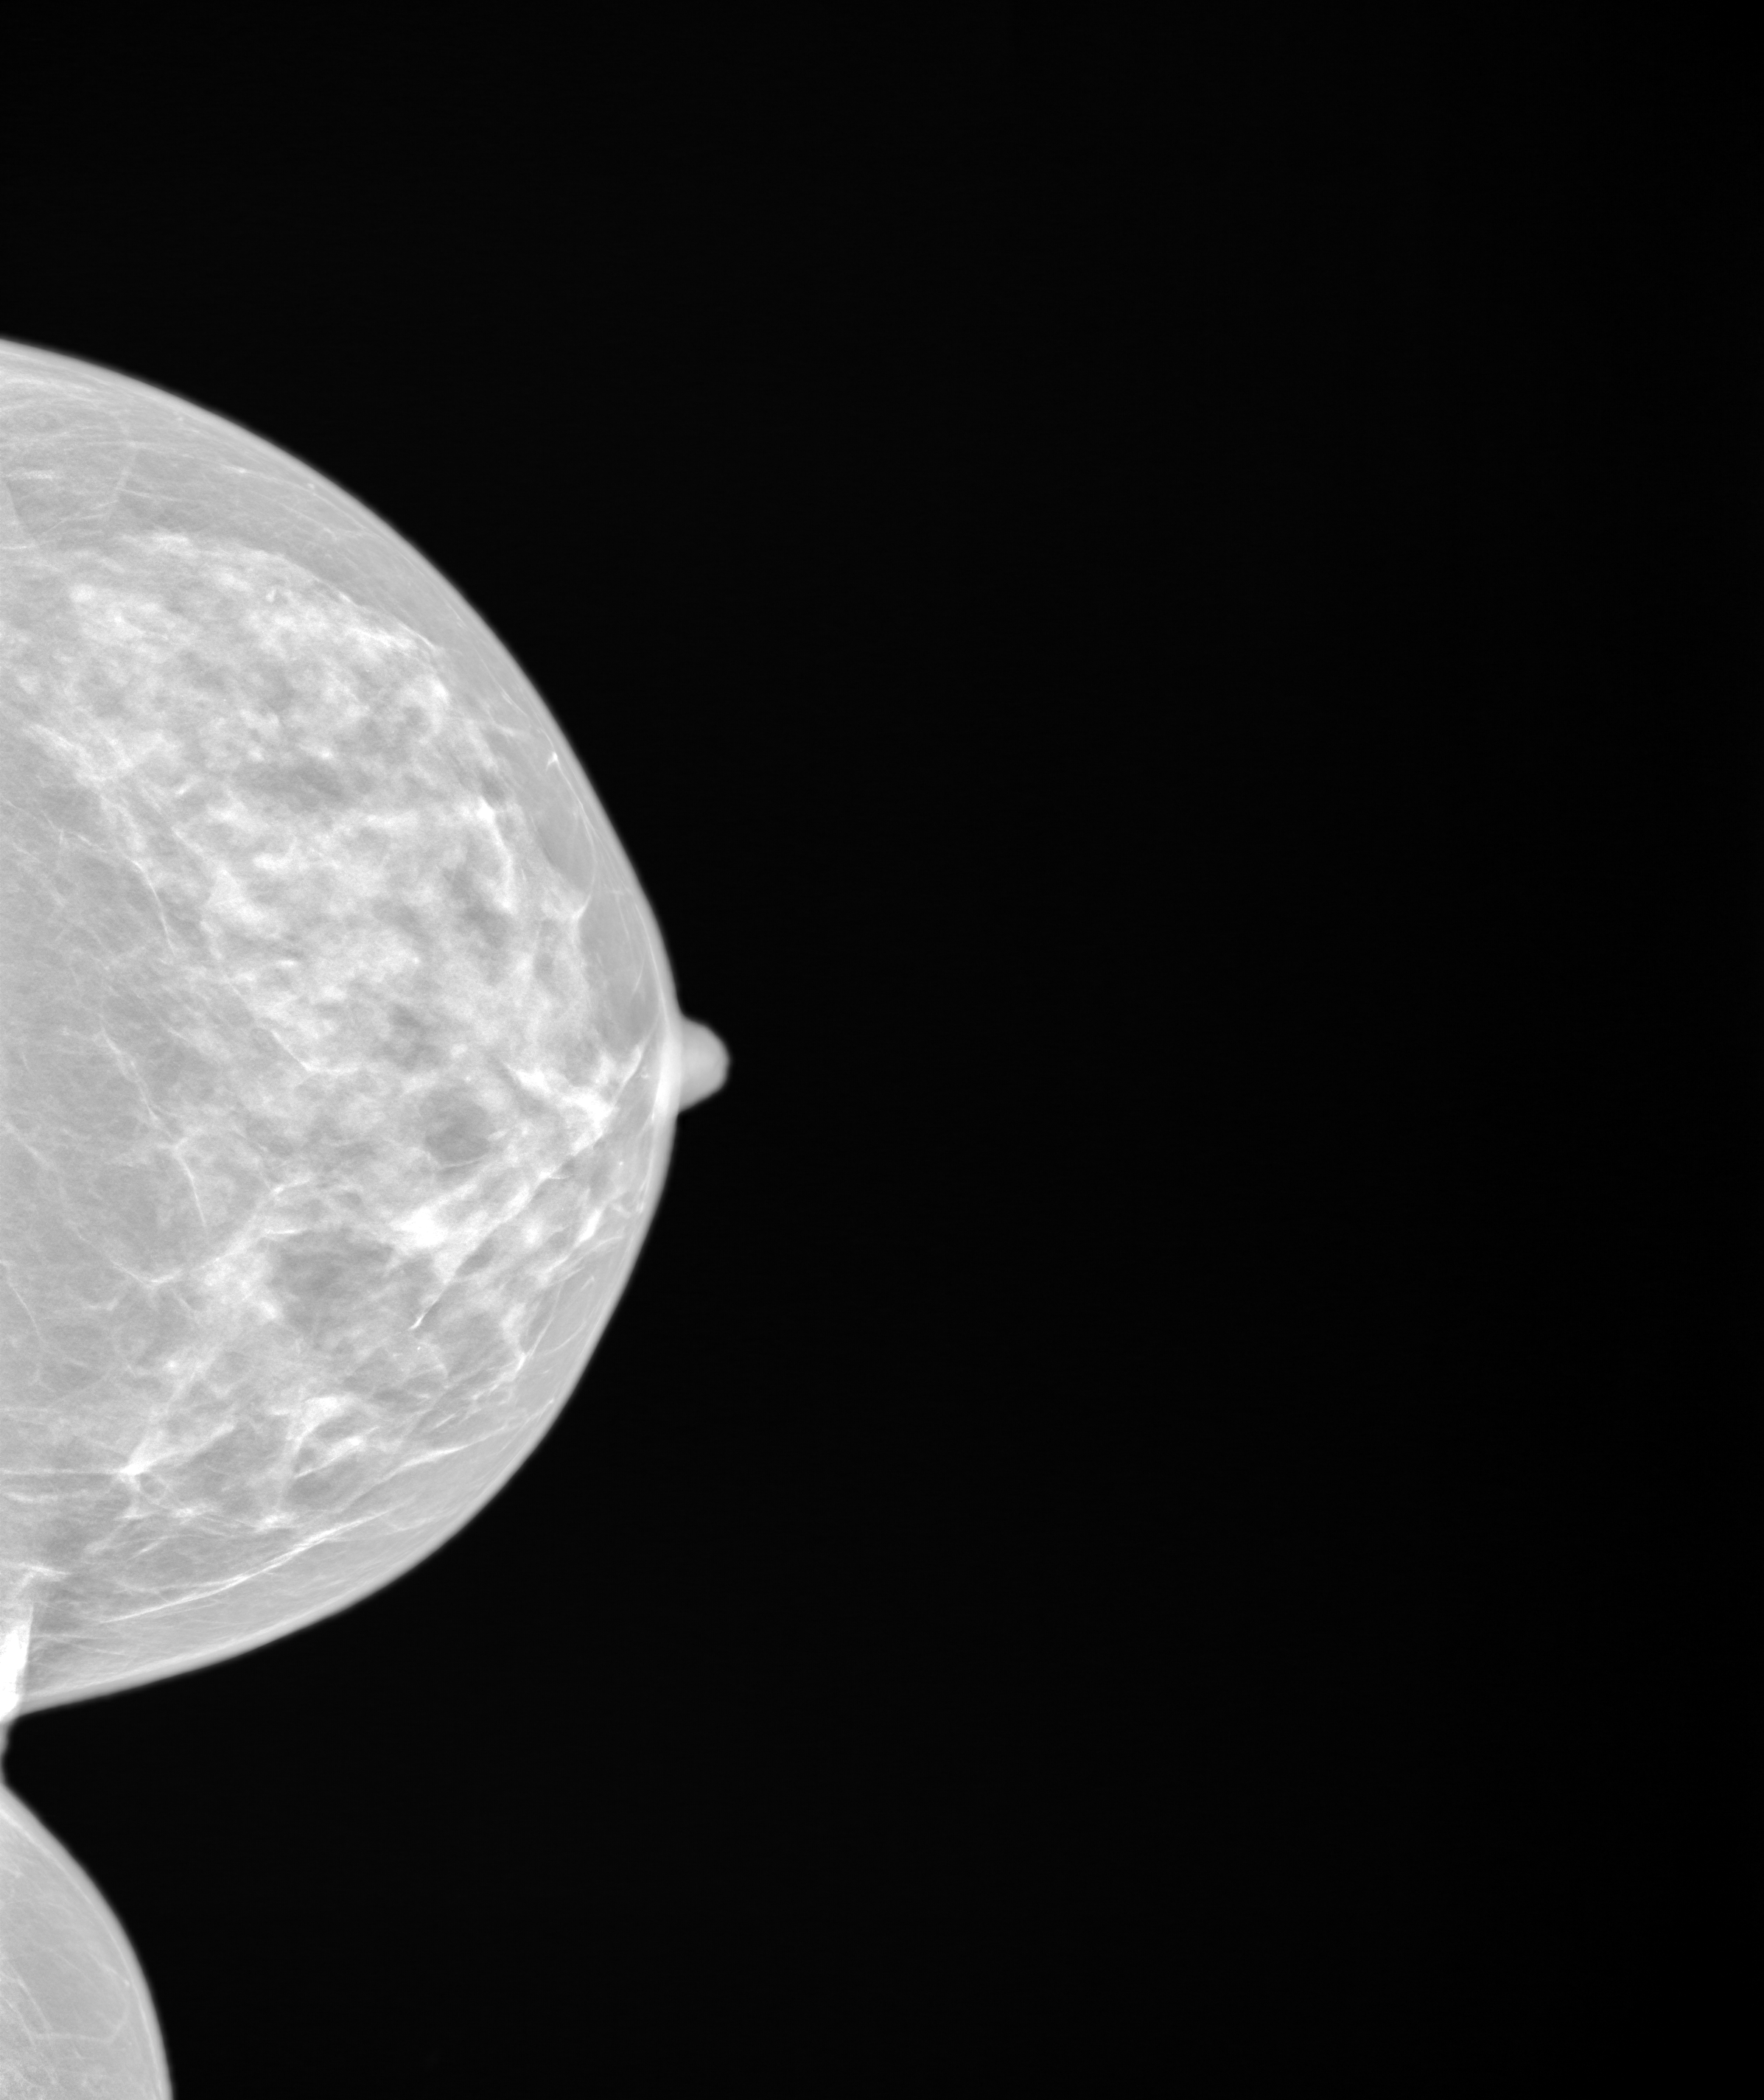
Annual screening mammography examination; system: SenoIris_1SP2(440). Female patient, age 59 years.
Image type: synthesized 2-D view from tomosynthesis. Breast: left. Projection: cranio-caudal projection.